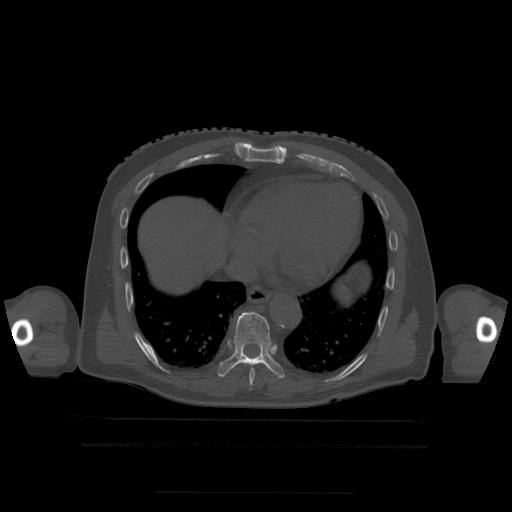
CT including the spine, one axial slice; slice 265 of 522 in the series (ordered by position); bone window (W 1800 / L 400 HU); 1.25 mm slice thickness; 512 × 512 image matrix, field of view 436 × 436 mm. Patient age 68 years. From the clinical record (not read from this slice): primary cancer: urothelial.
Structures marked on this image (semi-automatically segmented with operator editing):
- T7 vertebra: bounding box (x1, y1, x2, y2) in pixels: (250, 382, 253, 391)
- T8 vertebra: (250, 369, 255, 383)
- T9 vertebra: (218, 312, 285, 379)